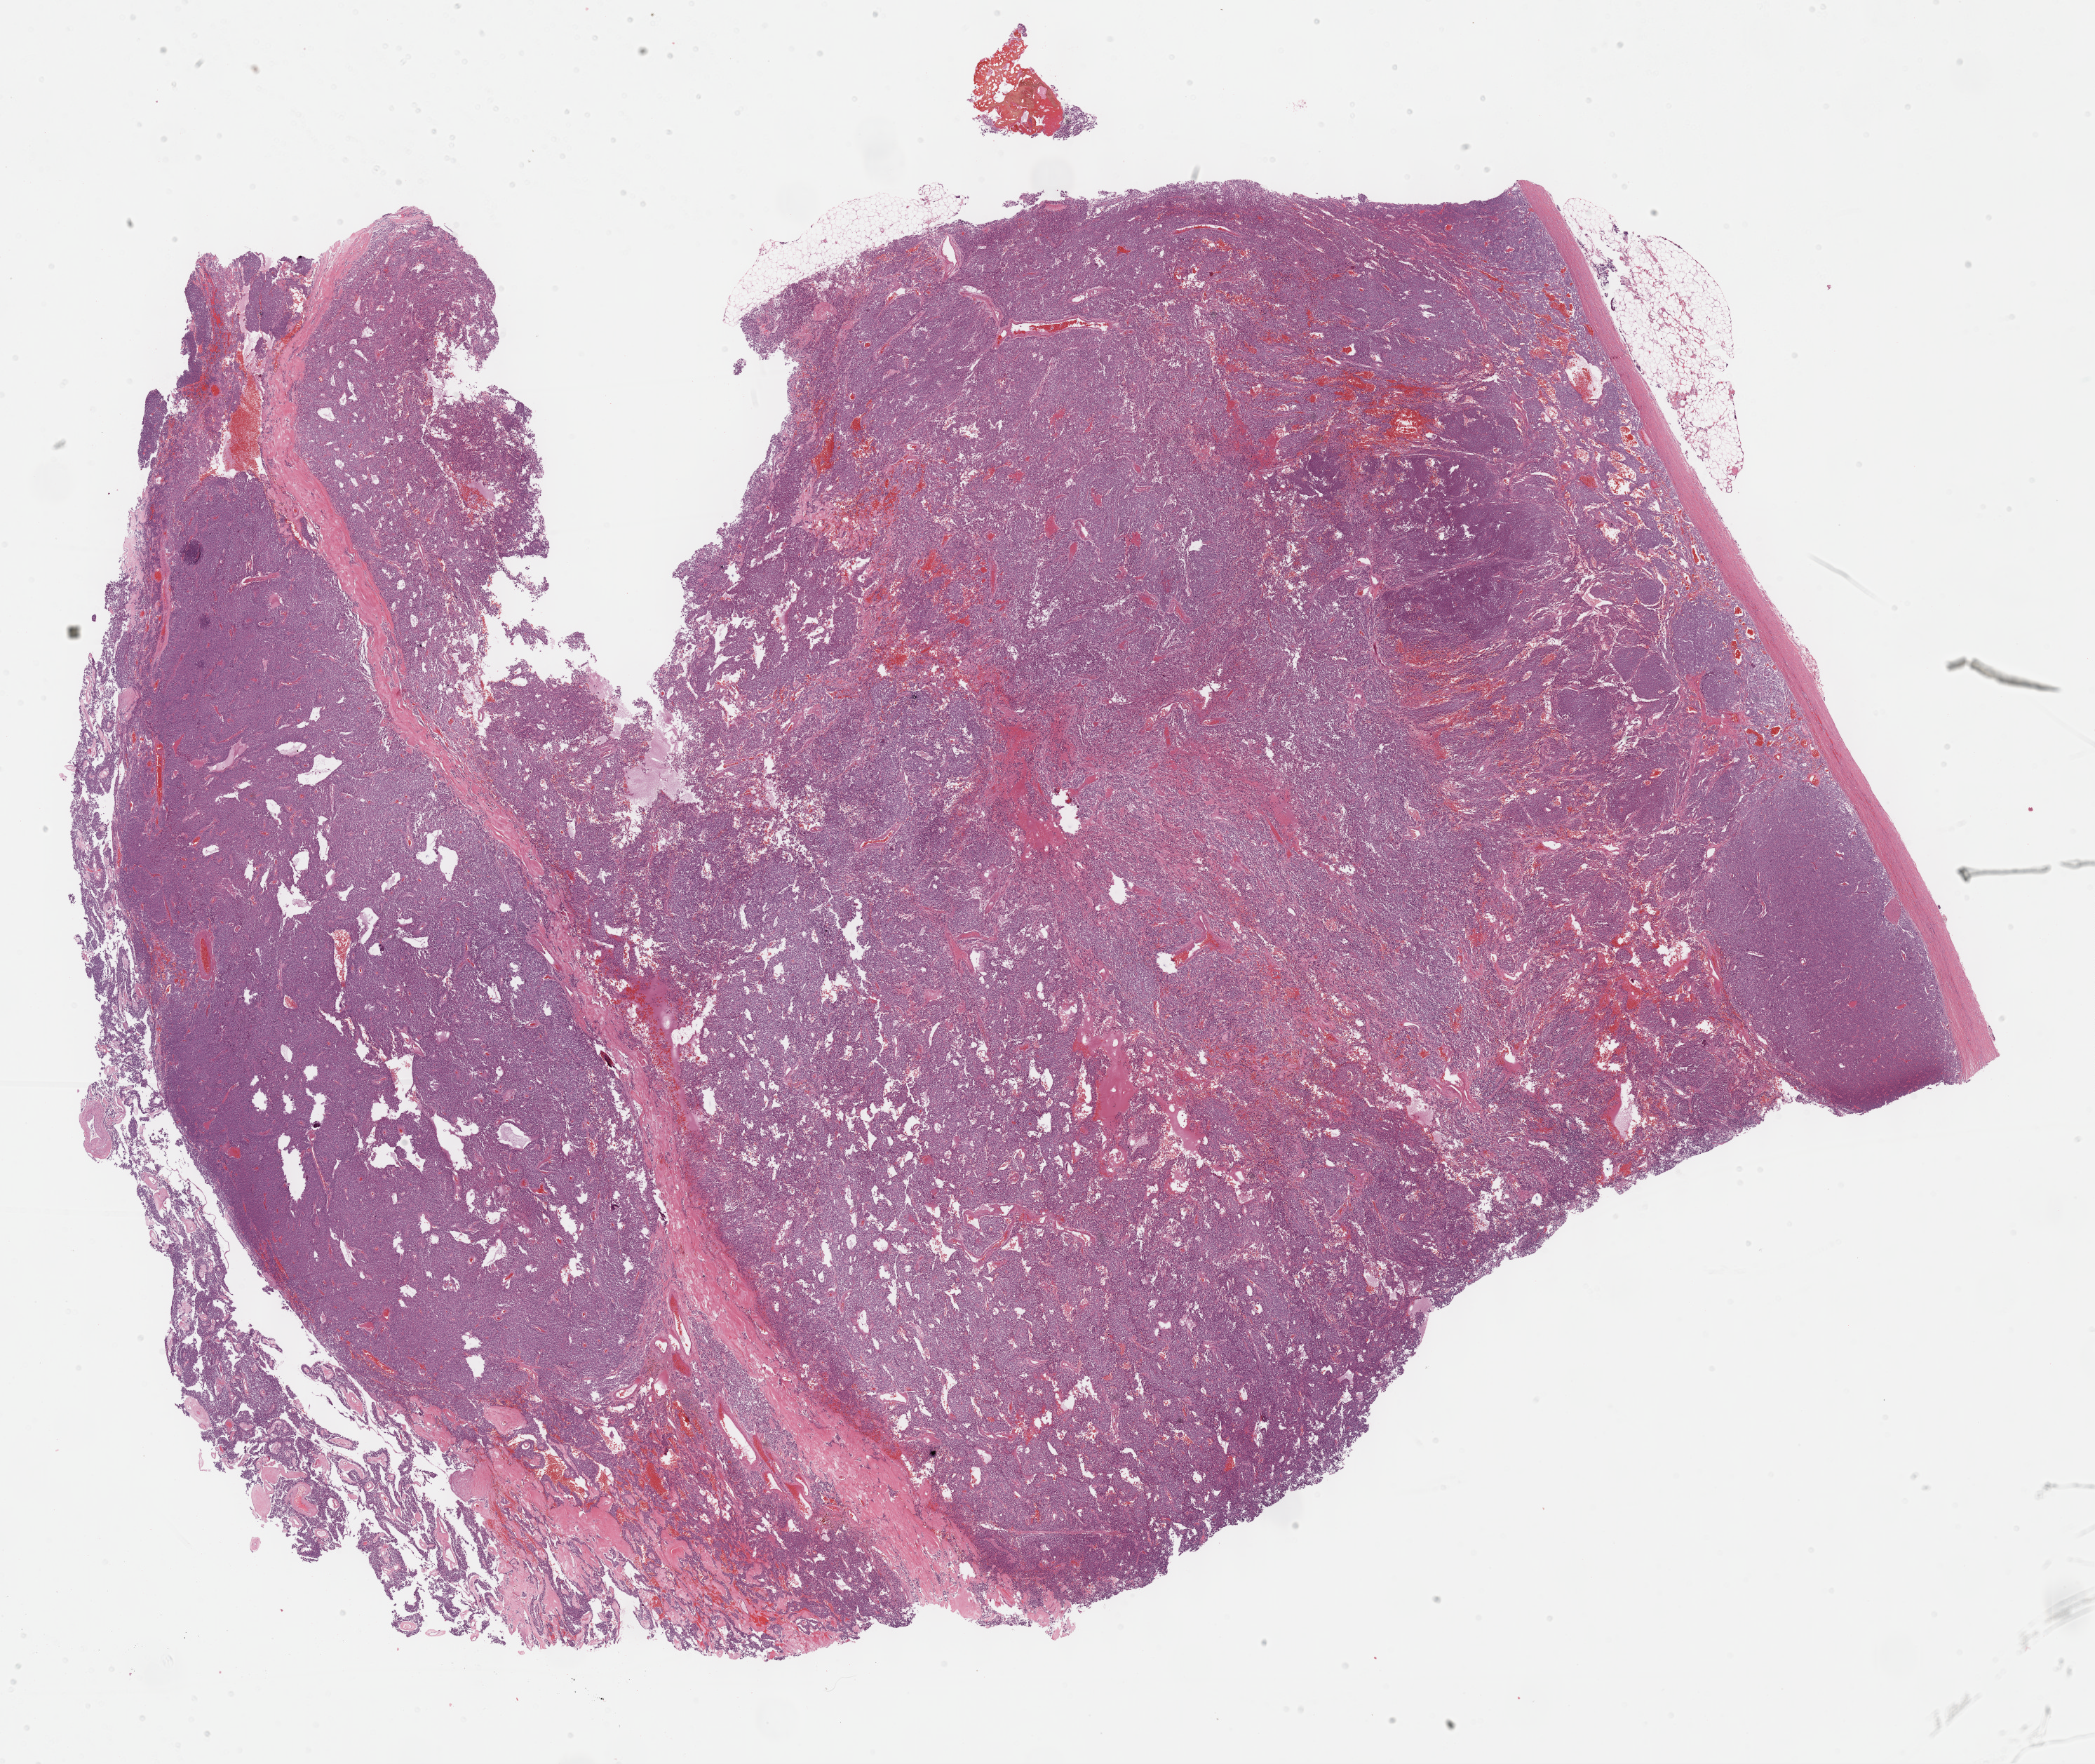
Hematoxylin and eosin (H&E) stained whole-slide image, low-resolution overview of the scanned area, about 24.2 x 20.3 mm; formalin-fixed paraffin-embedded (FFPE) diagnostic section; primary tumour sample from the adrenal gland. Male, age 56 years at initial diagnosis.
• laterality: right
• histologic diagnosis: Pheochromocytoma, NOS